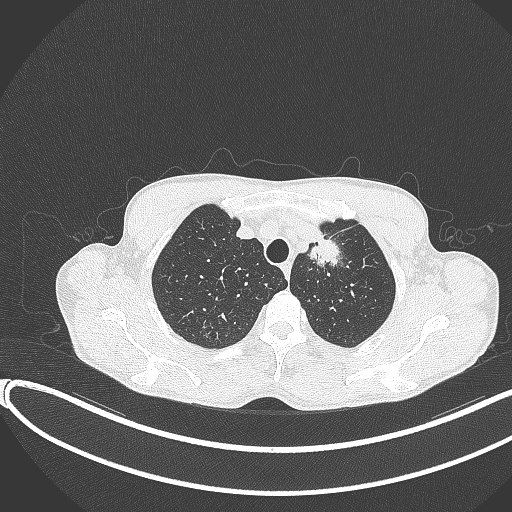
Chest CT, one axial slice. Position 323 of 374 along the scan axis. Reconstruction kernel B70f. 120 kVp. Lung window (W 1500 / L -600 HU). 1 mm slice thickness. 512 × 512 image matrix, field of view 400 × 400 mm. Patient: male, 58 years. From the clinical record (not read from this slice): clinical TNM (as recorded): T1c N1 M0.
Structures marked on this image (rectangle marked by the reading radiologist):
- lung tumour (recorded histology: adenocarcinoma): bounding box (x1, y1, x2, y2) in pixels: (298, 216, 341, 272)